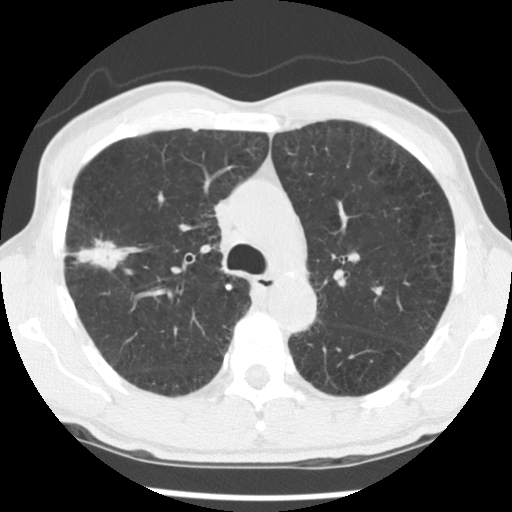
Low-dose screening chest CT, one axial slice. Slice 89 of 138 in the series (ordered by position). 140 kVp. Lung window (W 1500 / L -600 HU). 2.5 mm slice thickness. 512 × 512 image matrix, field of view 320 × 320 mm.
Annotated regions visible in this slice (expert manual segmentation):
- lesion 1 (tumor, upper lobe of right lung): bounding box [x1, y1, x2, y2] px = [73, 239, 142, 271]